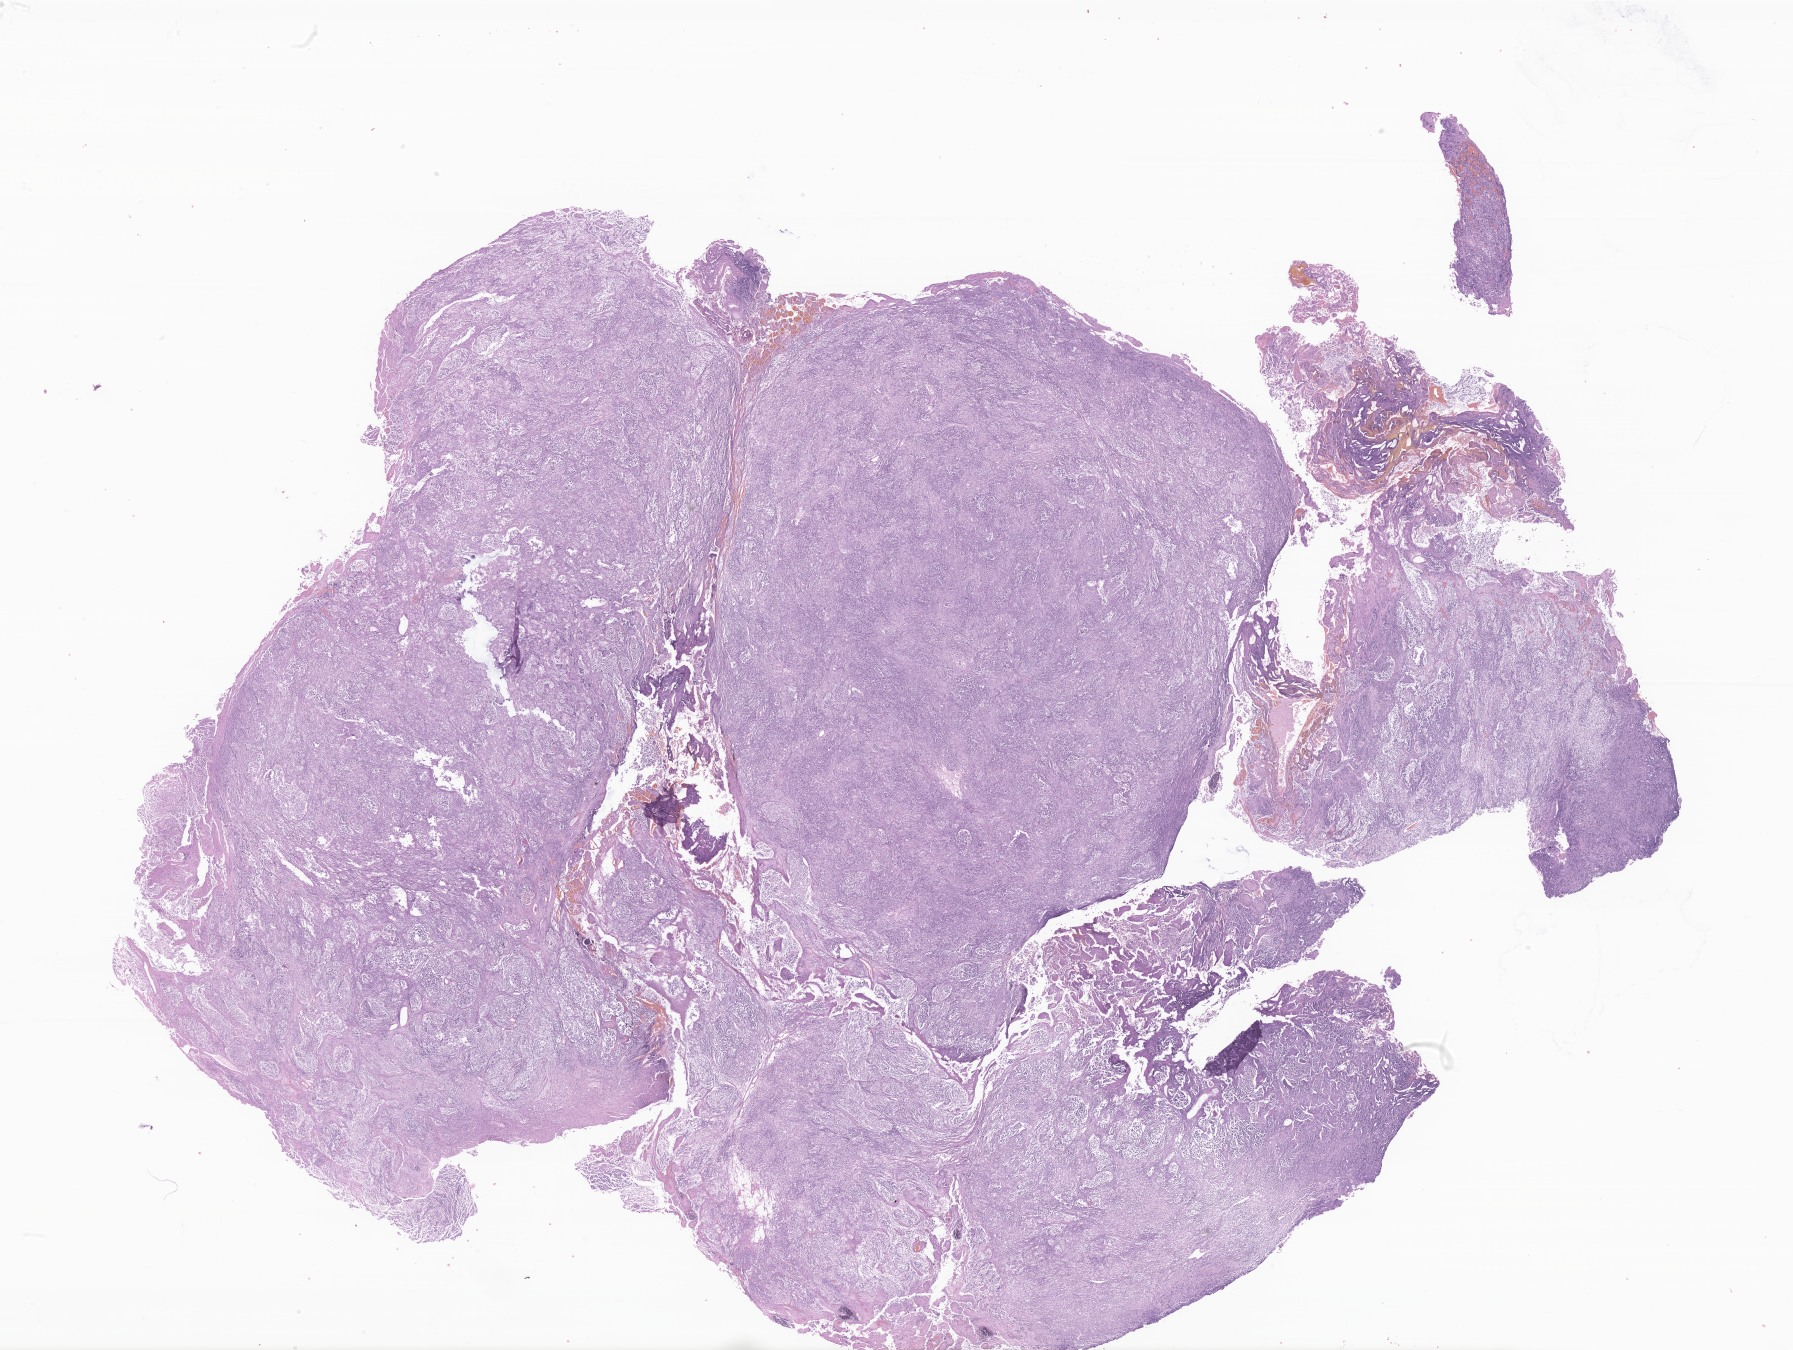
H&E whole-slide image of tumor tissue from the cerebellum, whole scanned area (about 30.2 x 22.8 mm) shown as a low-resolution overview; FFPE section. Male patient, age 340 days.
Diagnosis: Desmoplastic nodular medulloblastoma.